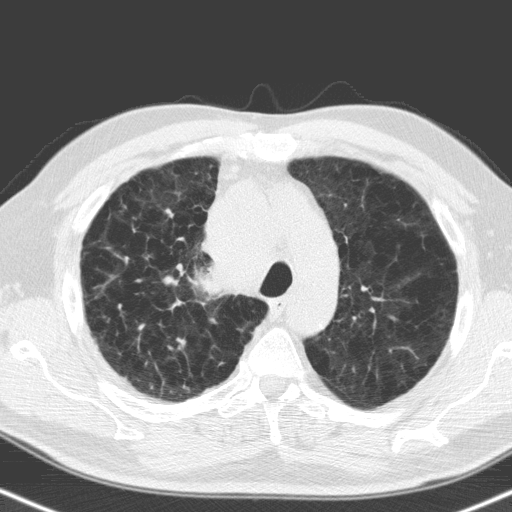
Low-dose screening chest CT, one axial slice; slice 126 of 160 in the series (ordered by position); 120 kVp; lung window (W 1500 / L -600 HU); 512 × 512 image matrix, field of view 324 × 324 mm.
Annotated regions visible in this slice (outlined manually by an expert reader):
- lesion 1 (tumor, hilum of right lung): box from (x=200, y=261) to (x=244, y=297) px